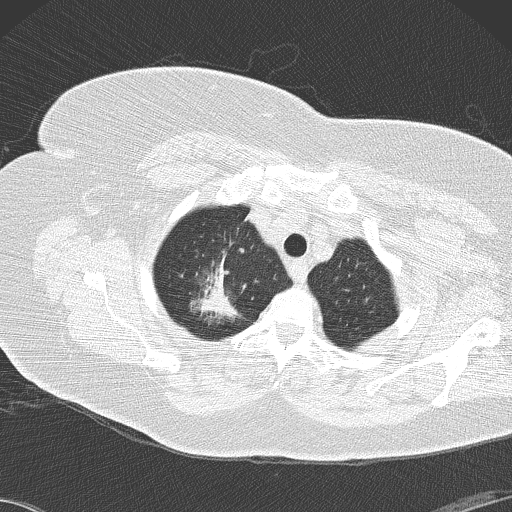
Axial slice from a low-dose chest CT screening exam, second screening round (one year after baseline), lung window (W 1500 / L -600 HU), 2 mm slice thickness, 512 × 512 image matrix, field of view 350 × 350 mm. Female participant, aged 72 years at enrolment. Former smoker at enrolment.
Lesion marked by an expert reader, bounding box <182,245,259,327> (left, top, right, bottom; pixels). The screening reader recorded 4 non-calcified nodules or masses ≥4 mm on this exam (right lower lobe, right lower lobe, right lower lobe, right upper lobe); which of them this box marks is not recorded. Official screen result: positive, other. Later outcome: lung cancer diagnosed 52 days after this screen — bronchiolo-alveolar adenocarcinoma, NOS, right upper lobe, stage IIIB (AJCC 6th edition), 45 mm at pathology.